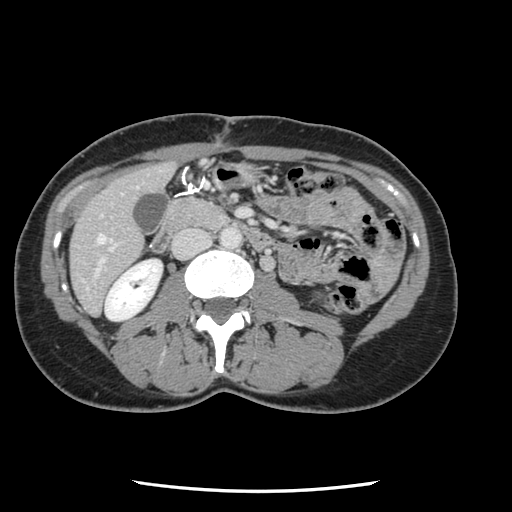
Contrast-enhanced abdominal CT, one axial slice. 120 kVp. Intravenous contrast given. Soft-tissue window (W 400 / L 40 HU). 2.5 mm slice thickness. 512 × 512 image matrix. Female patient, age 43 years. Case-level facts recorded for this patient, not image findings: diagnosis: colorectal cancer liver metastases, imaged before liver resection; multiple liver metastases: yes; largest metastasis: 3.4 cm.
Structures marked on this image (outlined manually by an expert reader):
- hepatic veins: bounding box <96,234,105,243> (left, top, right, bottom; pixels)
- liver: <71,164,174,315>
- planned liver remnant (the part of the liver to remain after resection): <71,164,174,314>